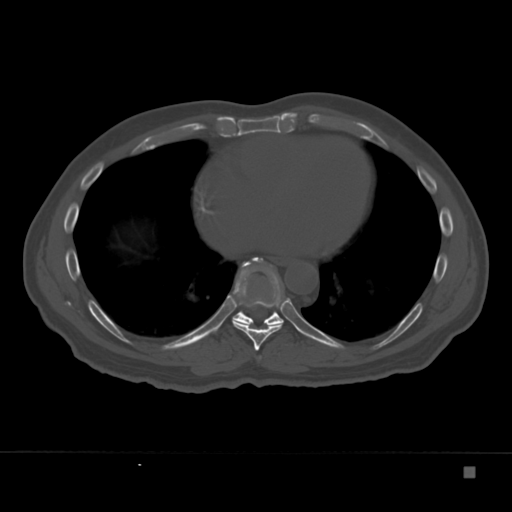
CT including the spine, one axial slice; slice 200 of 332 in the series (ordered by position); 120 kVp; bone window (W 1800 / L 400 HU); 1.5 mm slice thickness; 512 × 512 image matrix, field of view 389 × 389 mm. Male patient, age 72 years. From the clinical record (not read from this slice): primary cancer: skeletal.
Structures marked on this image (semi-automatic segmentation, software-assisted and operator-edited):
- T8 vertebra: box from (x=232, y=259) to (x=285, y=351) px
- T9 vertebra: (x=215, y=257)–(x=287, y=332)